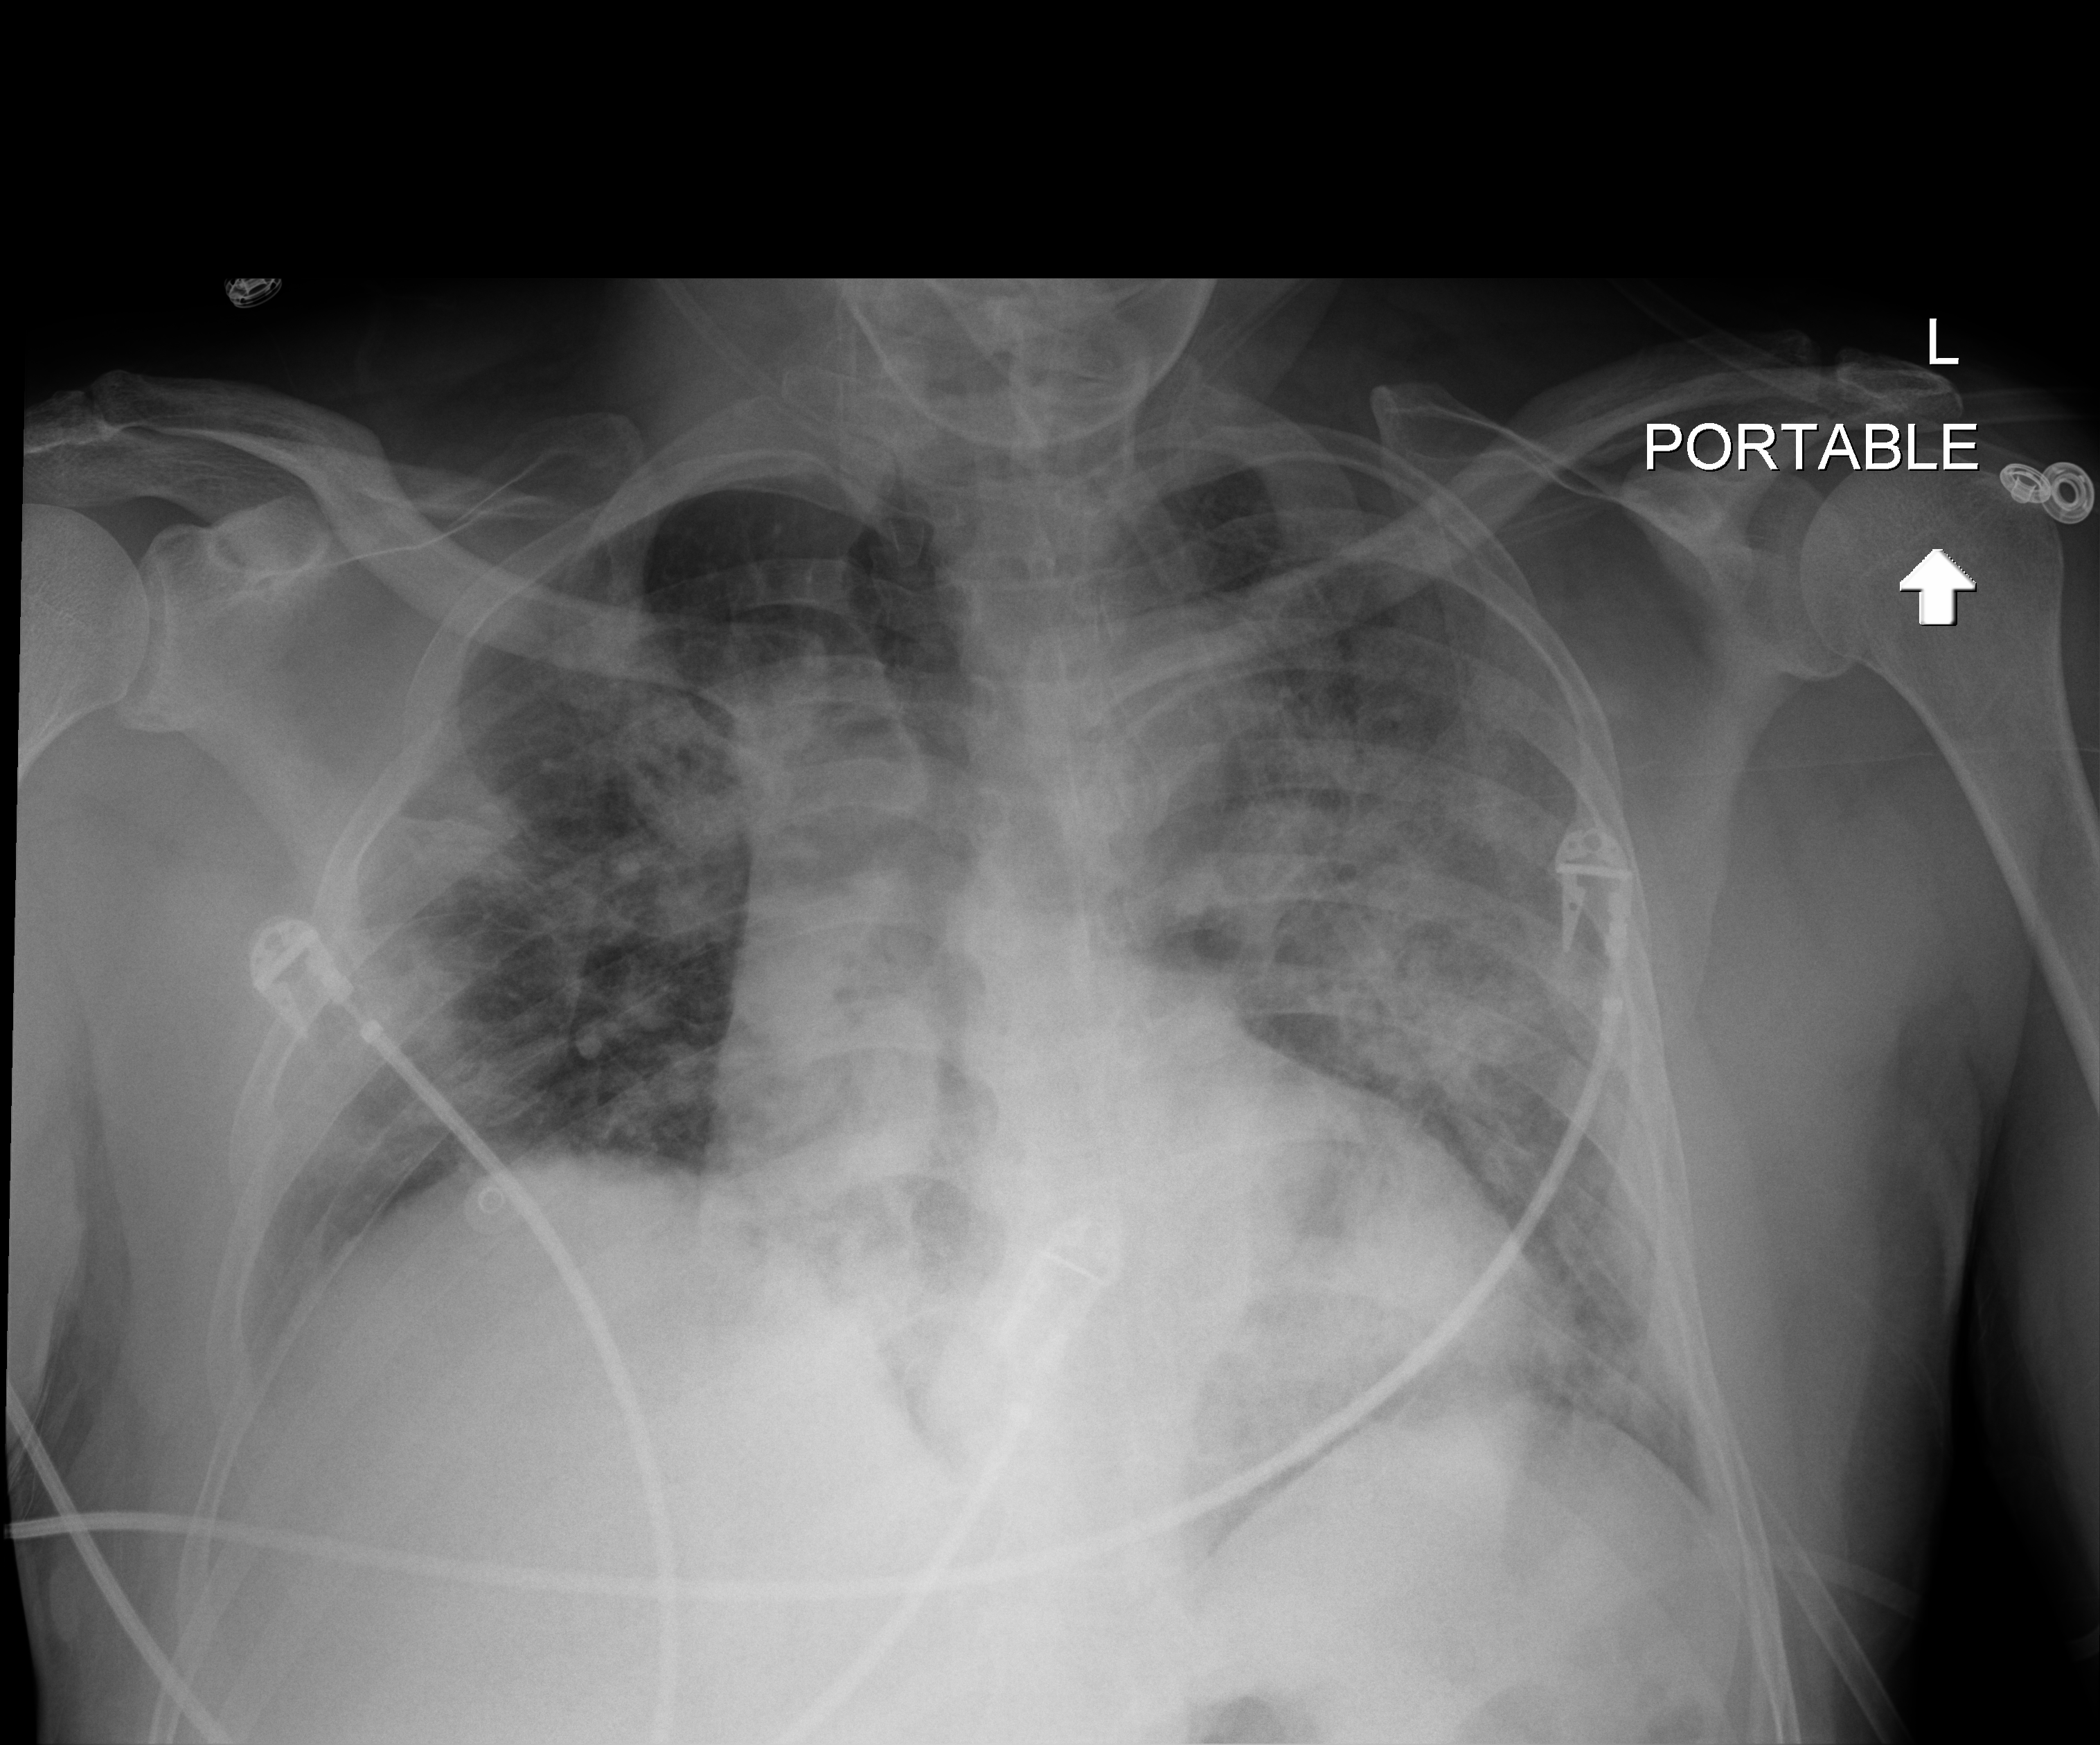
Chest X-ray (portable); anteroposterior (AP) projection. Male patient hospitalised with COVID-19, age 18–59 years.
Admission-level facts for this patient (not findings on this image; timing relative to this image not recorded): admitted to intensive care during this hospital stay: no; chronic kidney disease (admission record): no.